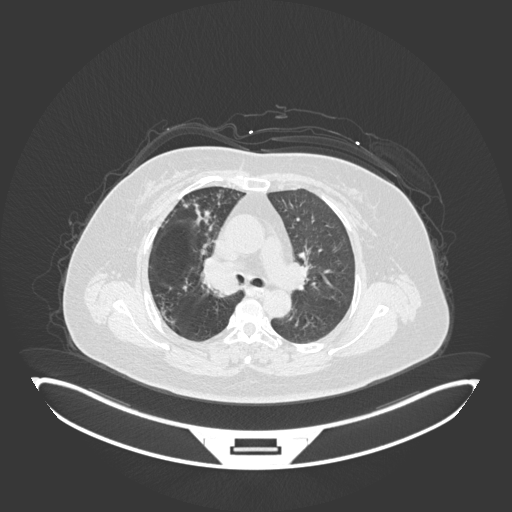
Chest CT, one axial slice. Slice 112 of 245 in the series (ordered by position). 120 kVp. Lung window (W 1500 / L -600 HU). 512 × 512 image matrix, field of view 500 × 500 mm. Patient: female, 60 years. From the clinical record (not read from this slice): clinical TNM (as recorded): T1c N0 M0; histopathological grade: G1-G2.
Structures marked on this image (bounding box drawn by a radiologist):
- lung tumour (recorded histology: squamous cell carcinoma): bounding box (x1, y1, x2, y2) in pixels: (195, 253, 242, 300)